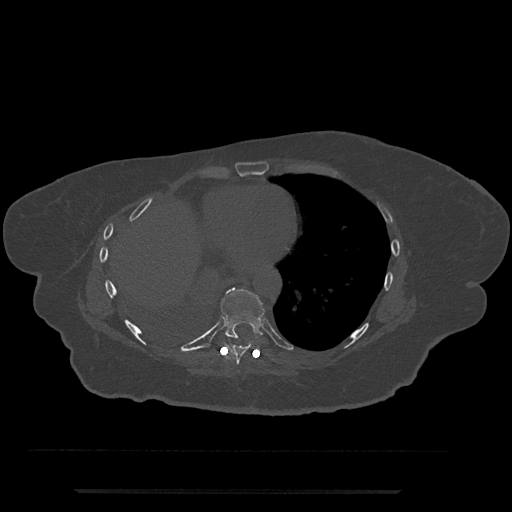
CT including the spine, one axial slice; position 363 of 797 along the scan axis; bone window (W 1800 / L 400 HU); 512 × 512 image matrix, field of view 440 × 440 mm. Patient: female, 51 years. From the clinical record (not read from this slice): primary cancer: neuro.
Outlined on this slice (semi-automatic segmentation, software-assisted and operator-edited):
- T8 vertebra: box from (x=229, y=340) to (x=249, y=365) px
- T9 vertebra: (x=221, y=287)–(x=265, y=341)